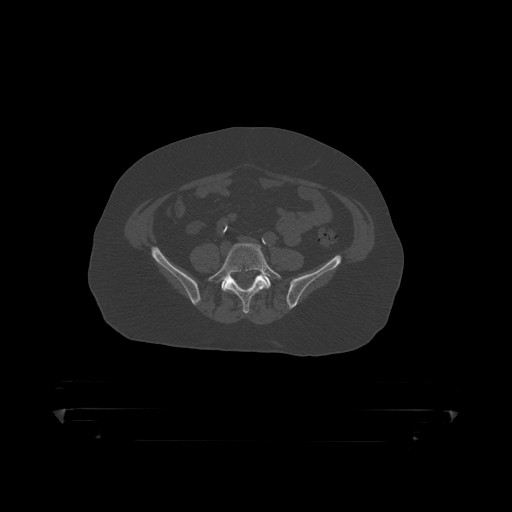
CT including the spine, one axial slice. Position 40 of 390 along the scan axis. Reconstruction kernel STANDARD. Bone window (W 1800 / L 400 HU). 512 × 512 image matrix, field of view 650 × 650 mm. Patient: male, 60 years. Case-level facts recorded for this patient, not image findings: primary cancer: prostate.
Annotated regions visible in this slice (semi-automatically segmented with operator editing):
- L5 vertebra: bounding box (x1, y1, x2, y2) in pixels: (208, 243, 282, 314)